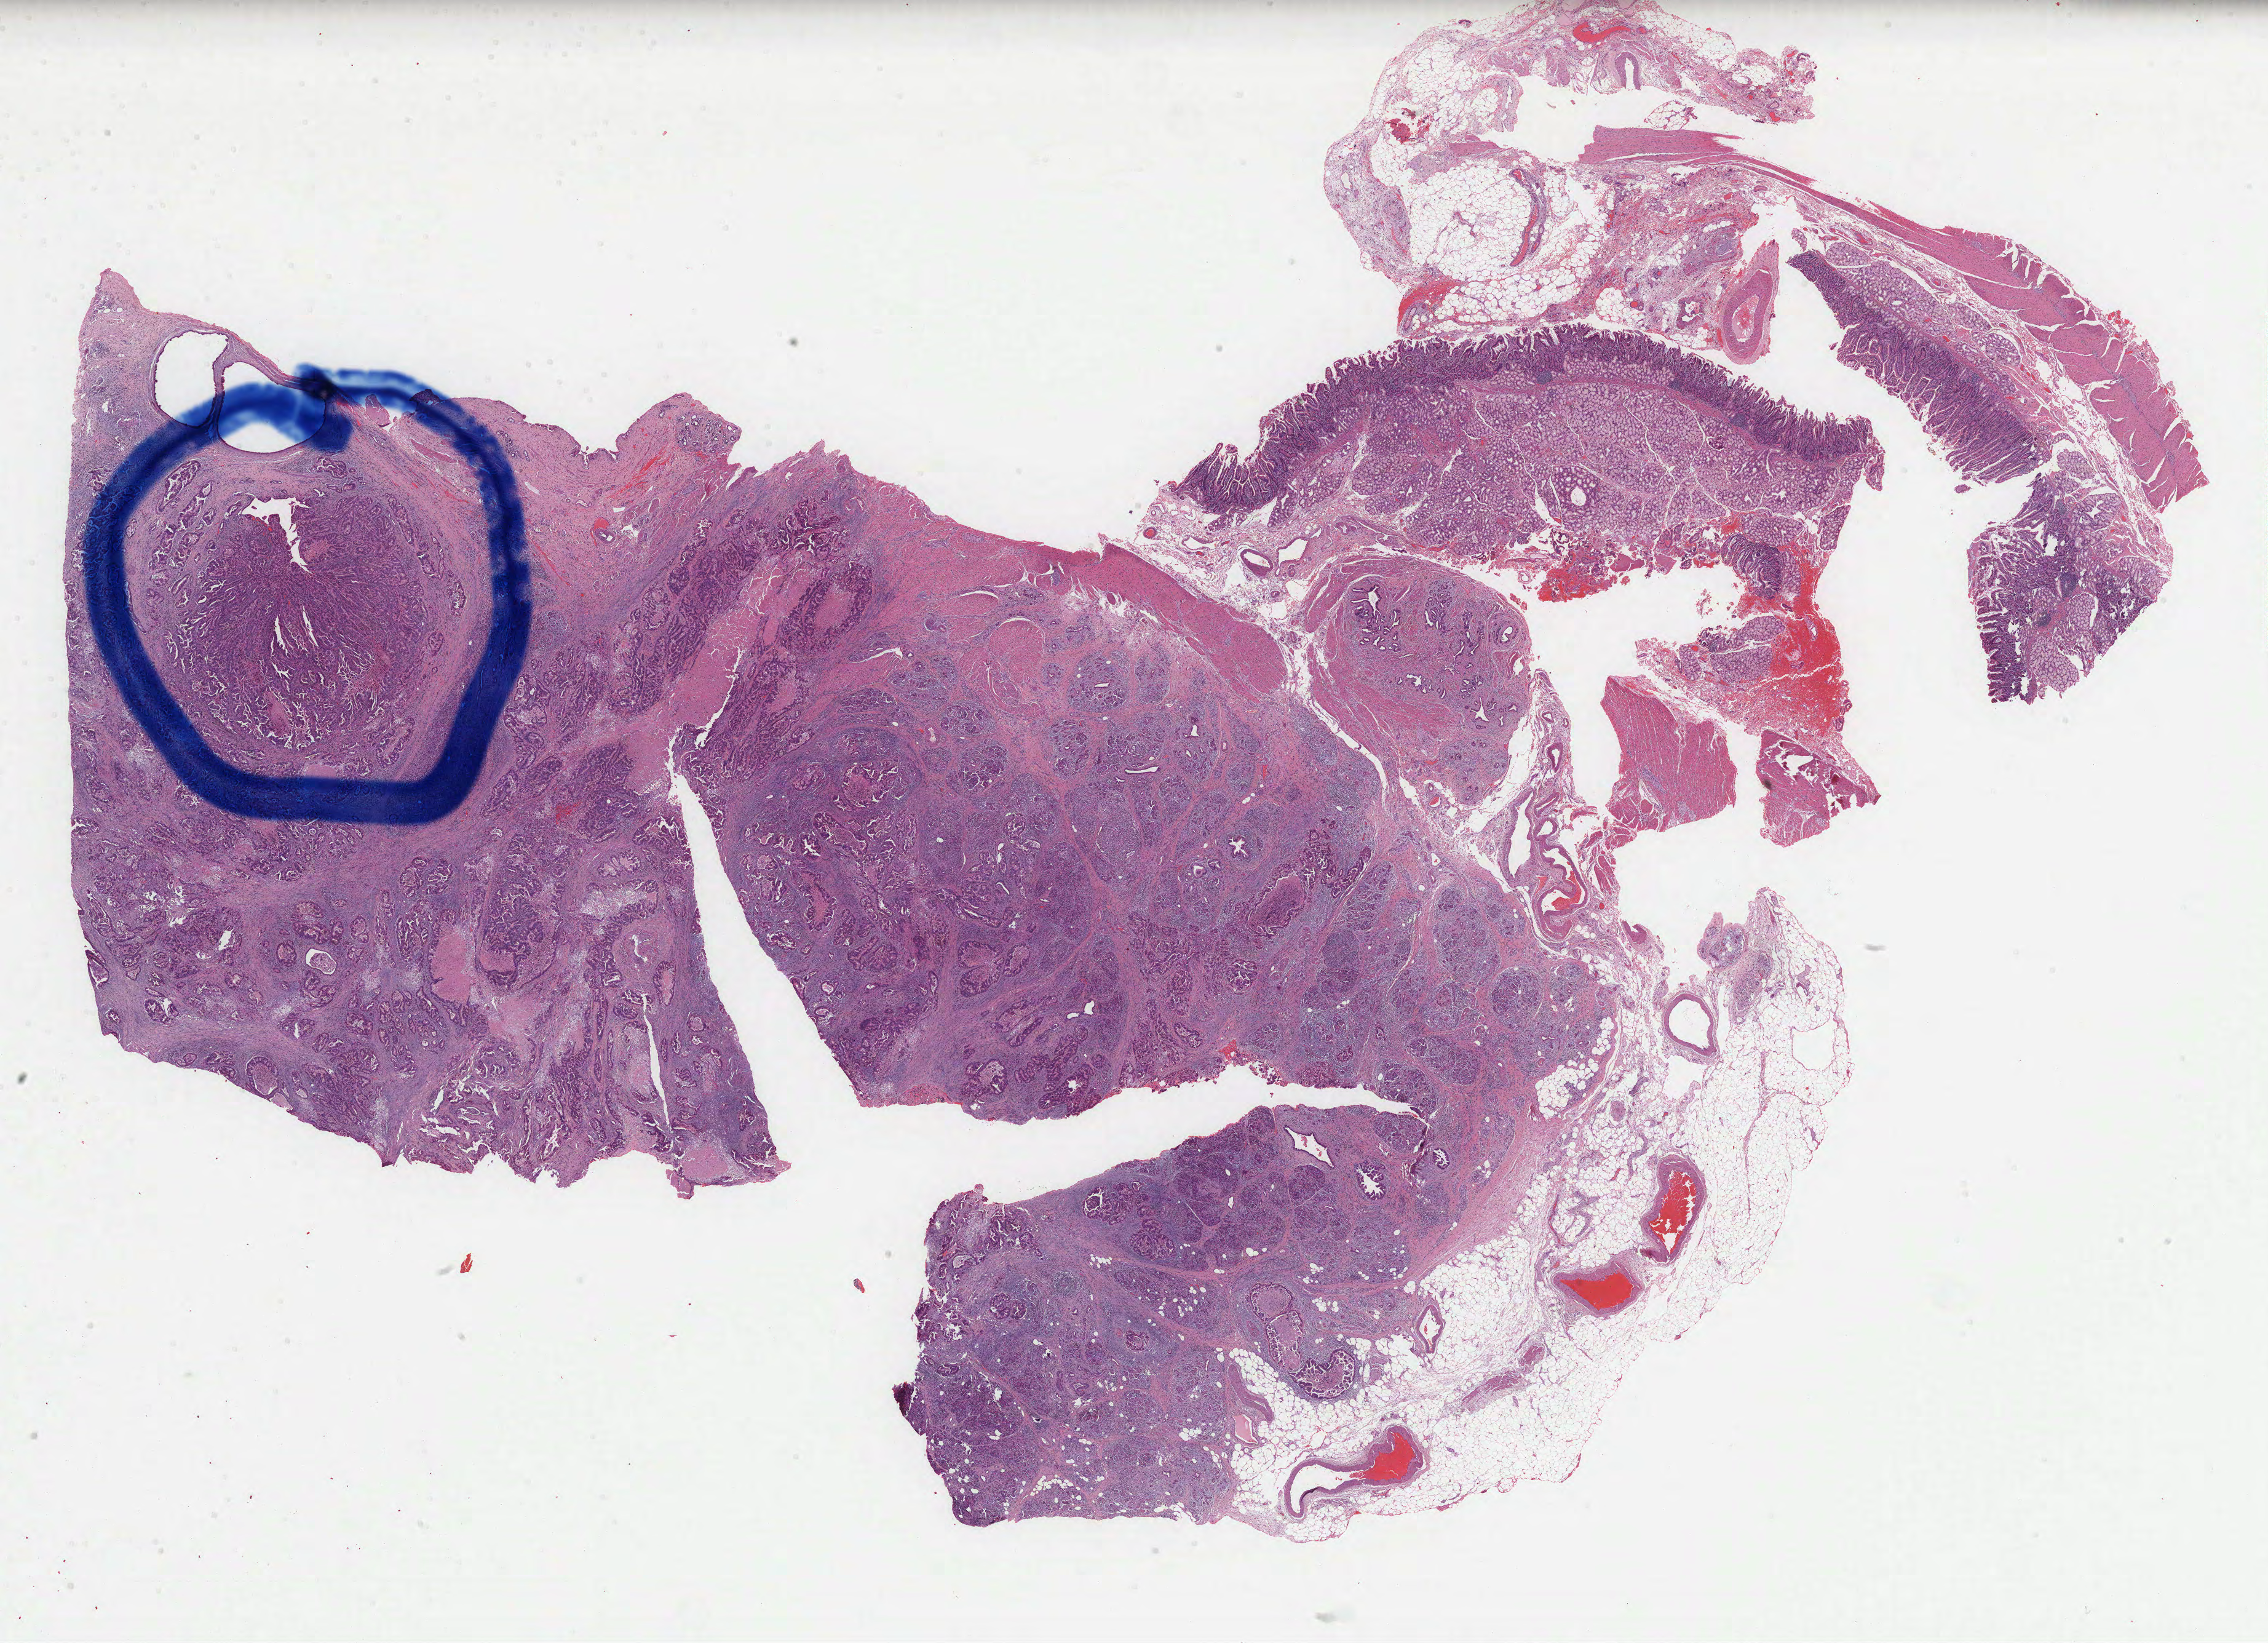
Digitized H&E-stained tissue section (whole slide), shown as a low-resolution overview of the whole scanned area (about 29.8 x 21.6 mm, slide scanned at 40x), formalin-fixed paraffin-embedded (FFPE) diagnostic section, sample: primary tumour, pancreas. Male, age 75 years at initial diagnosis. Histologic grade: G2 (moderately differentiated).
• pathologic diagnosis: Infiltrating duct carcinoma, NOS (head of pancreas)
• AJCC pathologic stage: IIB (7th edition)
• lymph nodes positive (case pathology): 5 of 14 examined